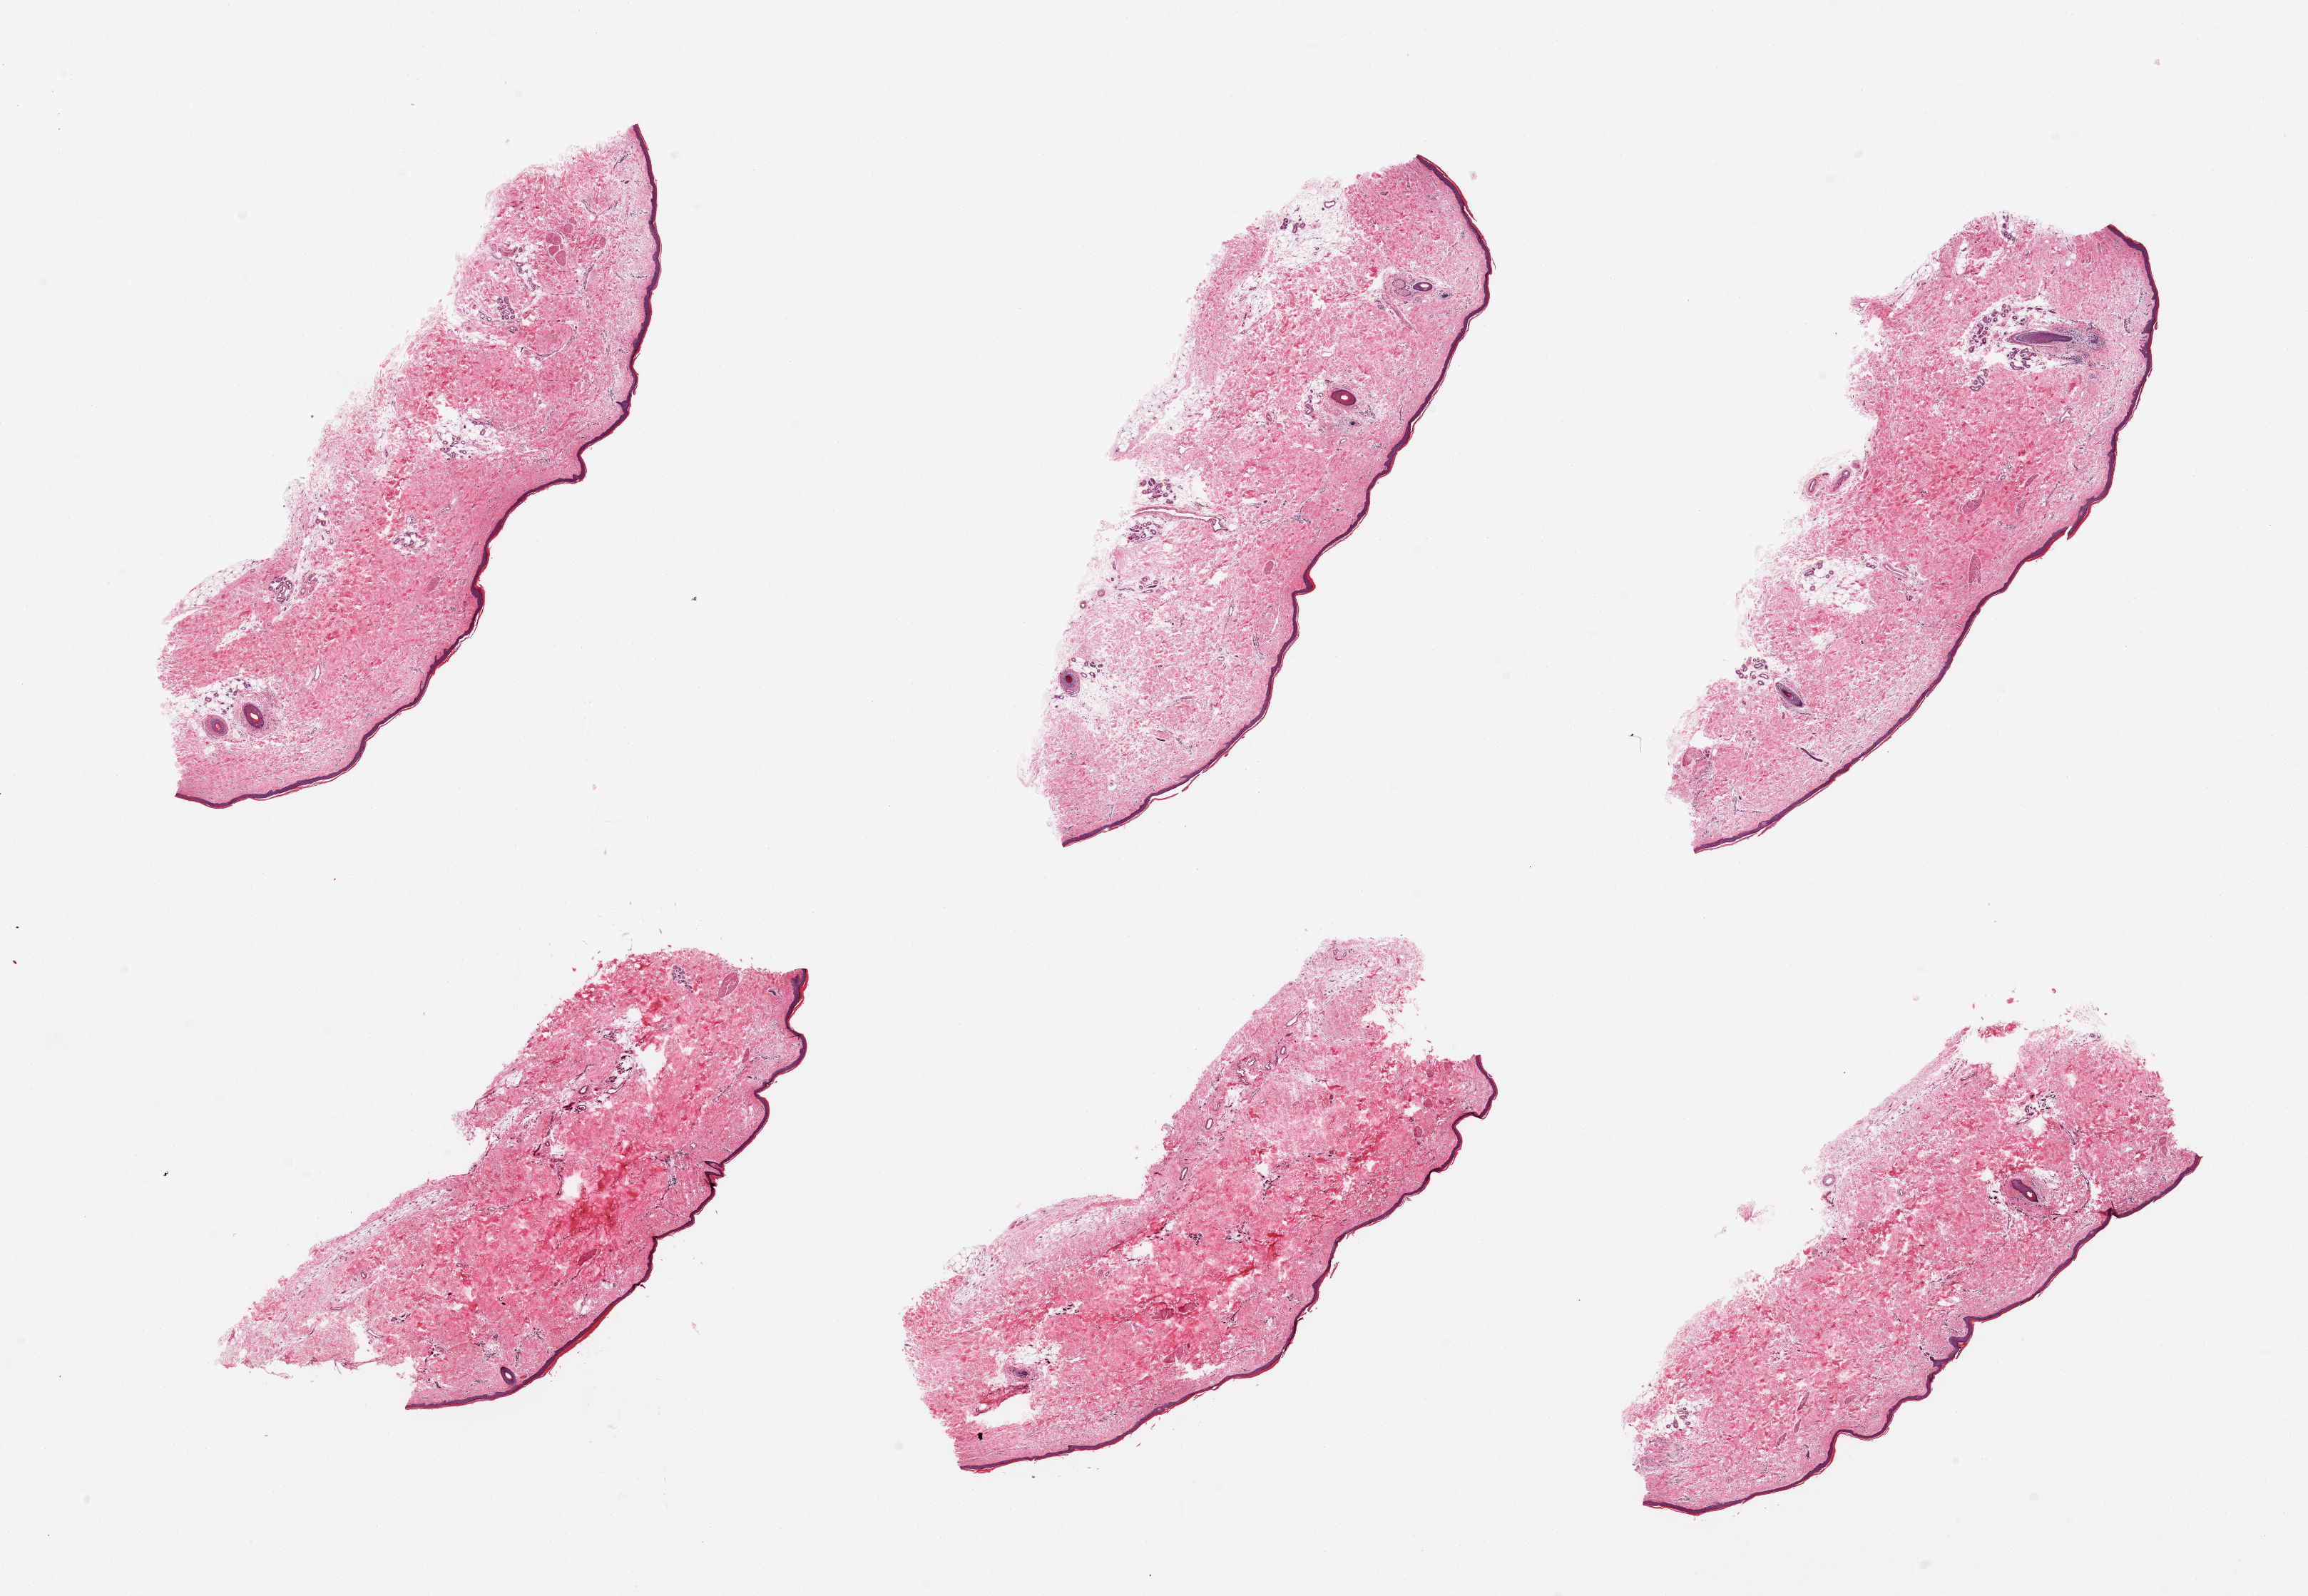
Digitized hematoxylin and eosin (H&E)-stained section, low-resolution overview of the scanned area, about 25.6 x 17.7 mm (from a 20x scan), PAXgene-fixed paraffin-embedded (PFPE) section, target tissue: skin of lower leg, tissue donor sample.
• review note (as recorded): 6 pieces; essentially well trimmed, epidermis measures 39 microns